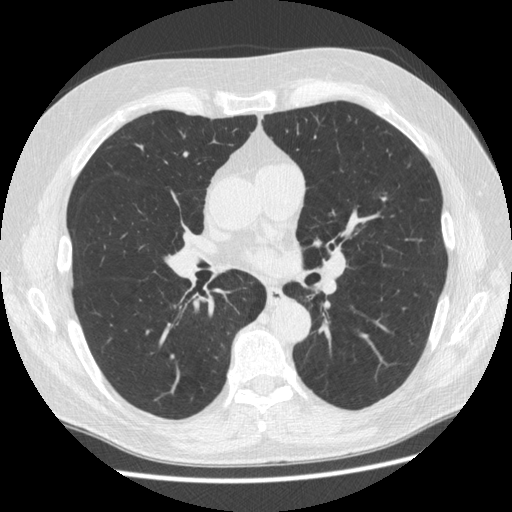
Low-dose screening chest CT, one axial slice; position 297 of 545 along the scan axis; reconstruction kernel STANDARD; lung window (W 1500 / L -600 HU); 1.25 mm slice thickness; 512 × 512 image matrix, field of view 360 × 360 mm.
Annotated regions visible in this slice (manually delineated by an expert):
- lesion 1 (nodule, upper lobe of left lung): box from (x=382, y=198) to (x=386, y=201) px